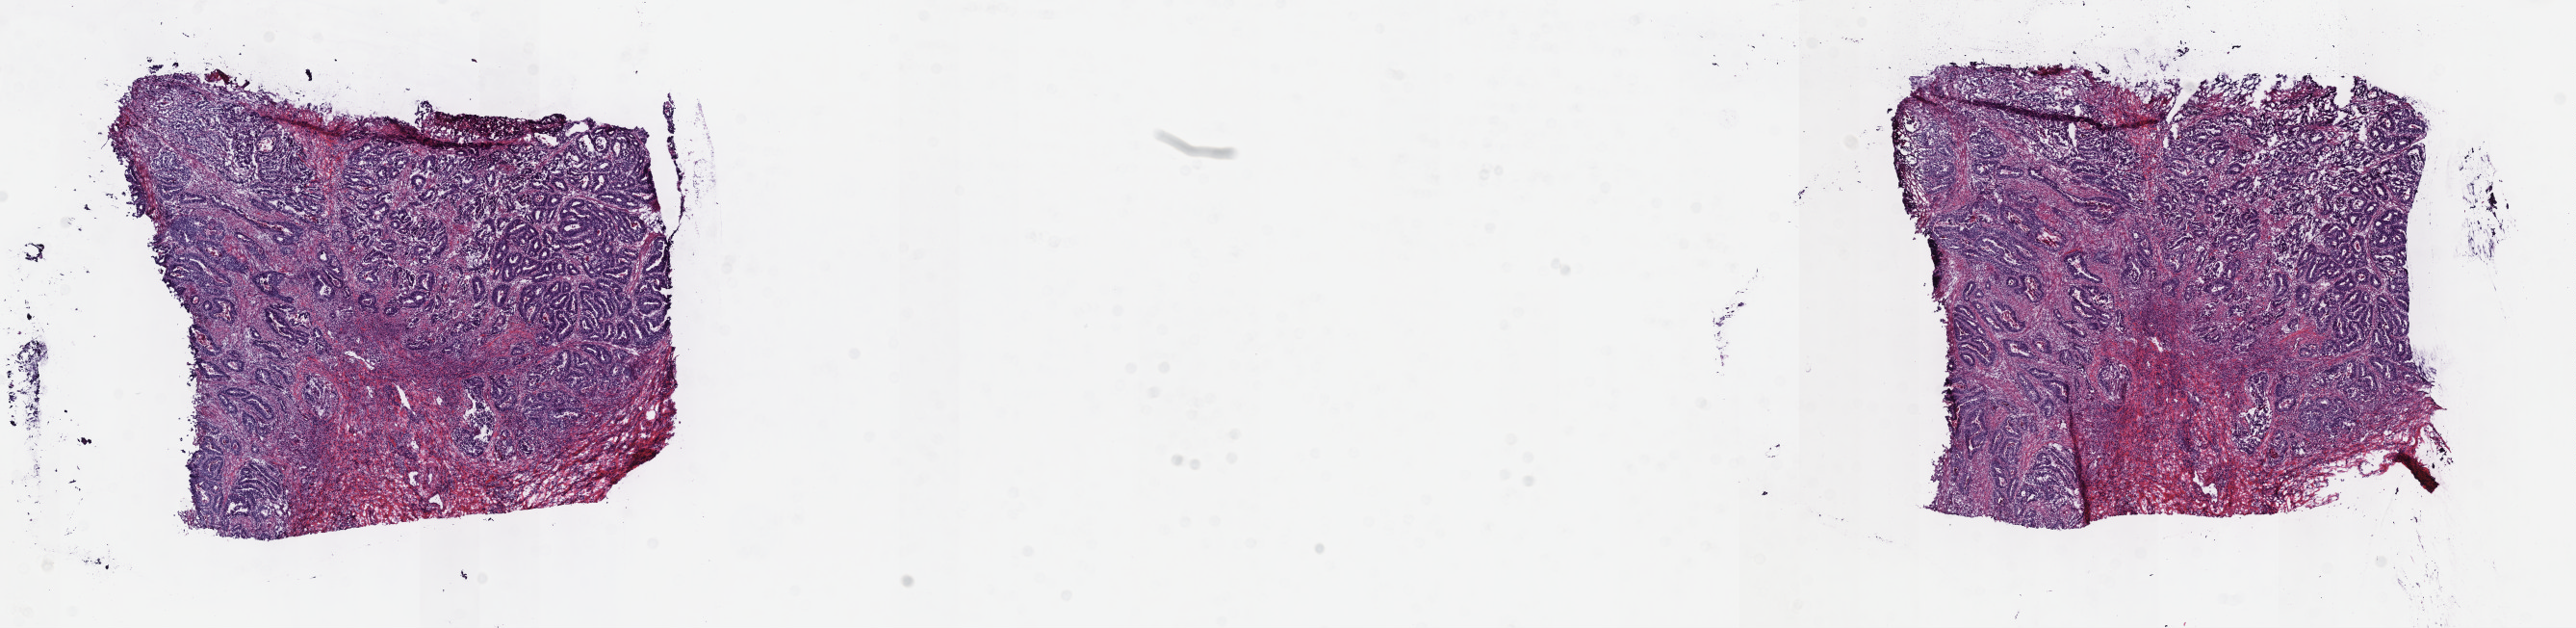
H&E whole-slide image — a low-resolution overview of the entire scanned area, about 21.6 x 5.3 mm. Frozen section from the top of the tissue portion. Sample: primary tumour, stomach. Male, age 70 years at initial diagnosis. Histologic grade: G2 (moderately differentiated). Slide review estimates, as recorded: tumour cells 60%, tumour nuclei 70%, normal cells 20%, stromal cells 20%, necrosis 0%. Inflammatory infiltration, as recorded: lymphocyte infiltration 0%, monocyte infiltration 0%, neutrophil infiltration 0%.
• pathologic diagnosis: Tubular adenocarcinoma (gastric antrum)
• AJCC pathologic stage: IV
• TNM: T4 N1 M0
• lymph nodes positive (case pathology): 1 of 16 examined